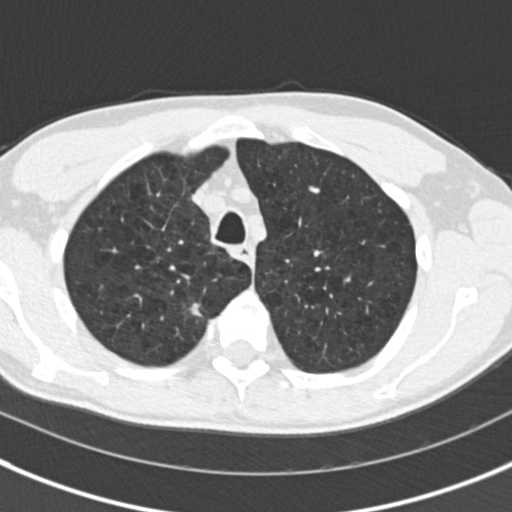
Low-dose screening chest CT, one axial slice; position 139 of 175 along the scan axis; reconstruction kernel B30f; lung window (W 1500 / L -600 HU); 2 mm slice thickness; 512 × 512 image matrix, field of view 306 × 306 mm.
Outlined on this slice (expert manual segmentation):
- lesion 2 (tumor, upper lobe of right lung): bounding box [x1, y1, x2, y2] px = [190, 303, 202, 317]